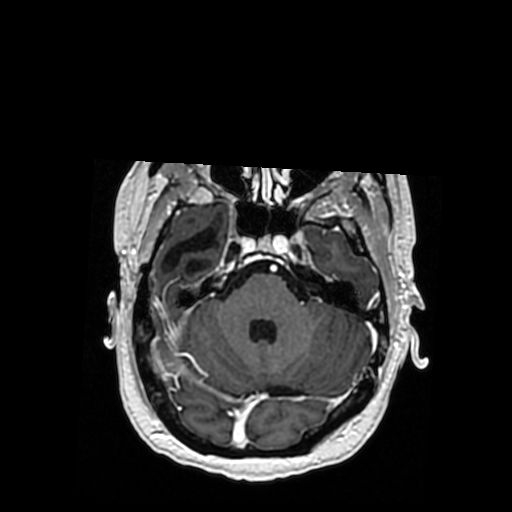
Brain MRI from a brain-tumour surgery series, one axial slice; position 249 of 364 along the scan axis; T1-weighted post-contrast; 0.5 mm slice thickness; 512 × 512 image matrix, field of view 260 × 260 mm. From the clinical record (not read from this slice): histopathology: Oligodendroglioma; WHO grade: 3; IDH mutation: yes; tumour location: Right Posterior Temporal Inferior Parietal.
Annotated regions visible in this slice (outlined manually by an expert reader):
- previous resection cavity: bounding box (x1, y1, x2, y2) in pixels: (163, 226, 218, 276)